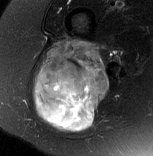
MRI of an extremity soft-tissue mass, one axial slice; slice 45 of 77 in the series (ordered by position); T2-weighted fat-saturated; MR volume resampled by the dataset authors to the PET/CT grid (not the native acquisition matrix); 3.27 mm slice thickness; 153 × 156 image matrix, field of view 149 × 152 mm. Female patient. Case-level facts recorded for this patient, not image findings: histological type: synovial sarcoma; grade: intermediate; site of the primary tumour: right buttock.
Outlined on this slice (expert contour drawn on MRI and transferred to this co-registered scan by the dataset authors):
- gross tumour volume including surrounding oedema: box from (x=33, y=40) to (x=109, y=132) px
- gross tumour volume (mass): (x=33, y=40)–(x=109, y=132)